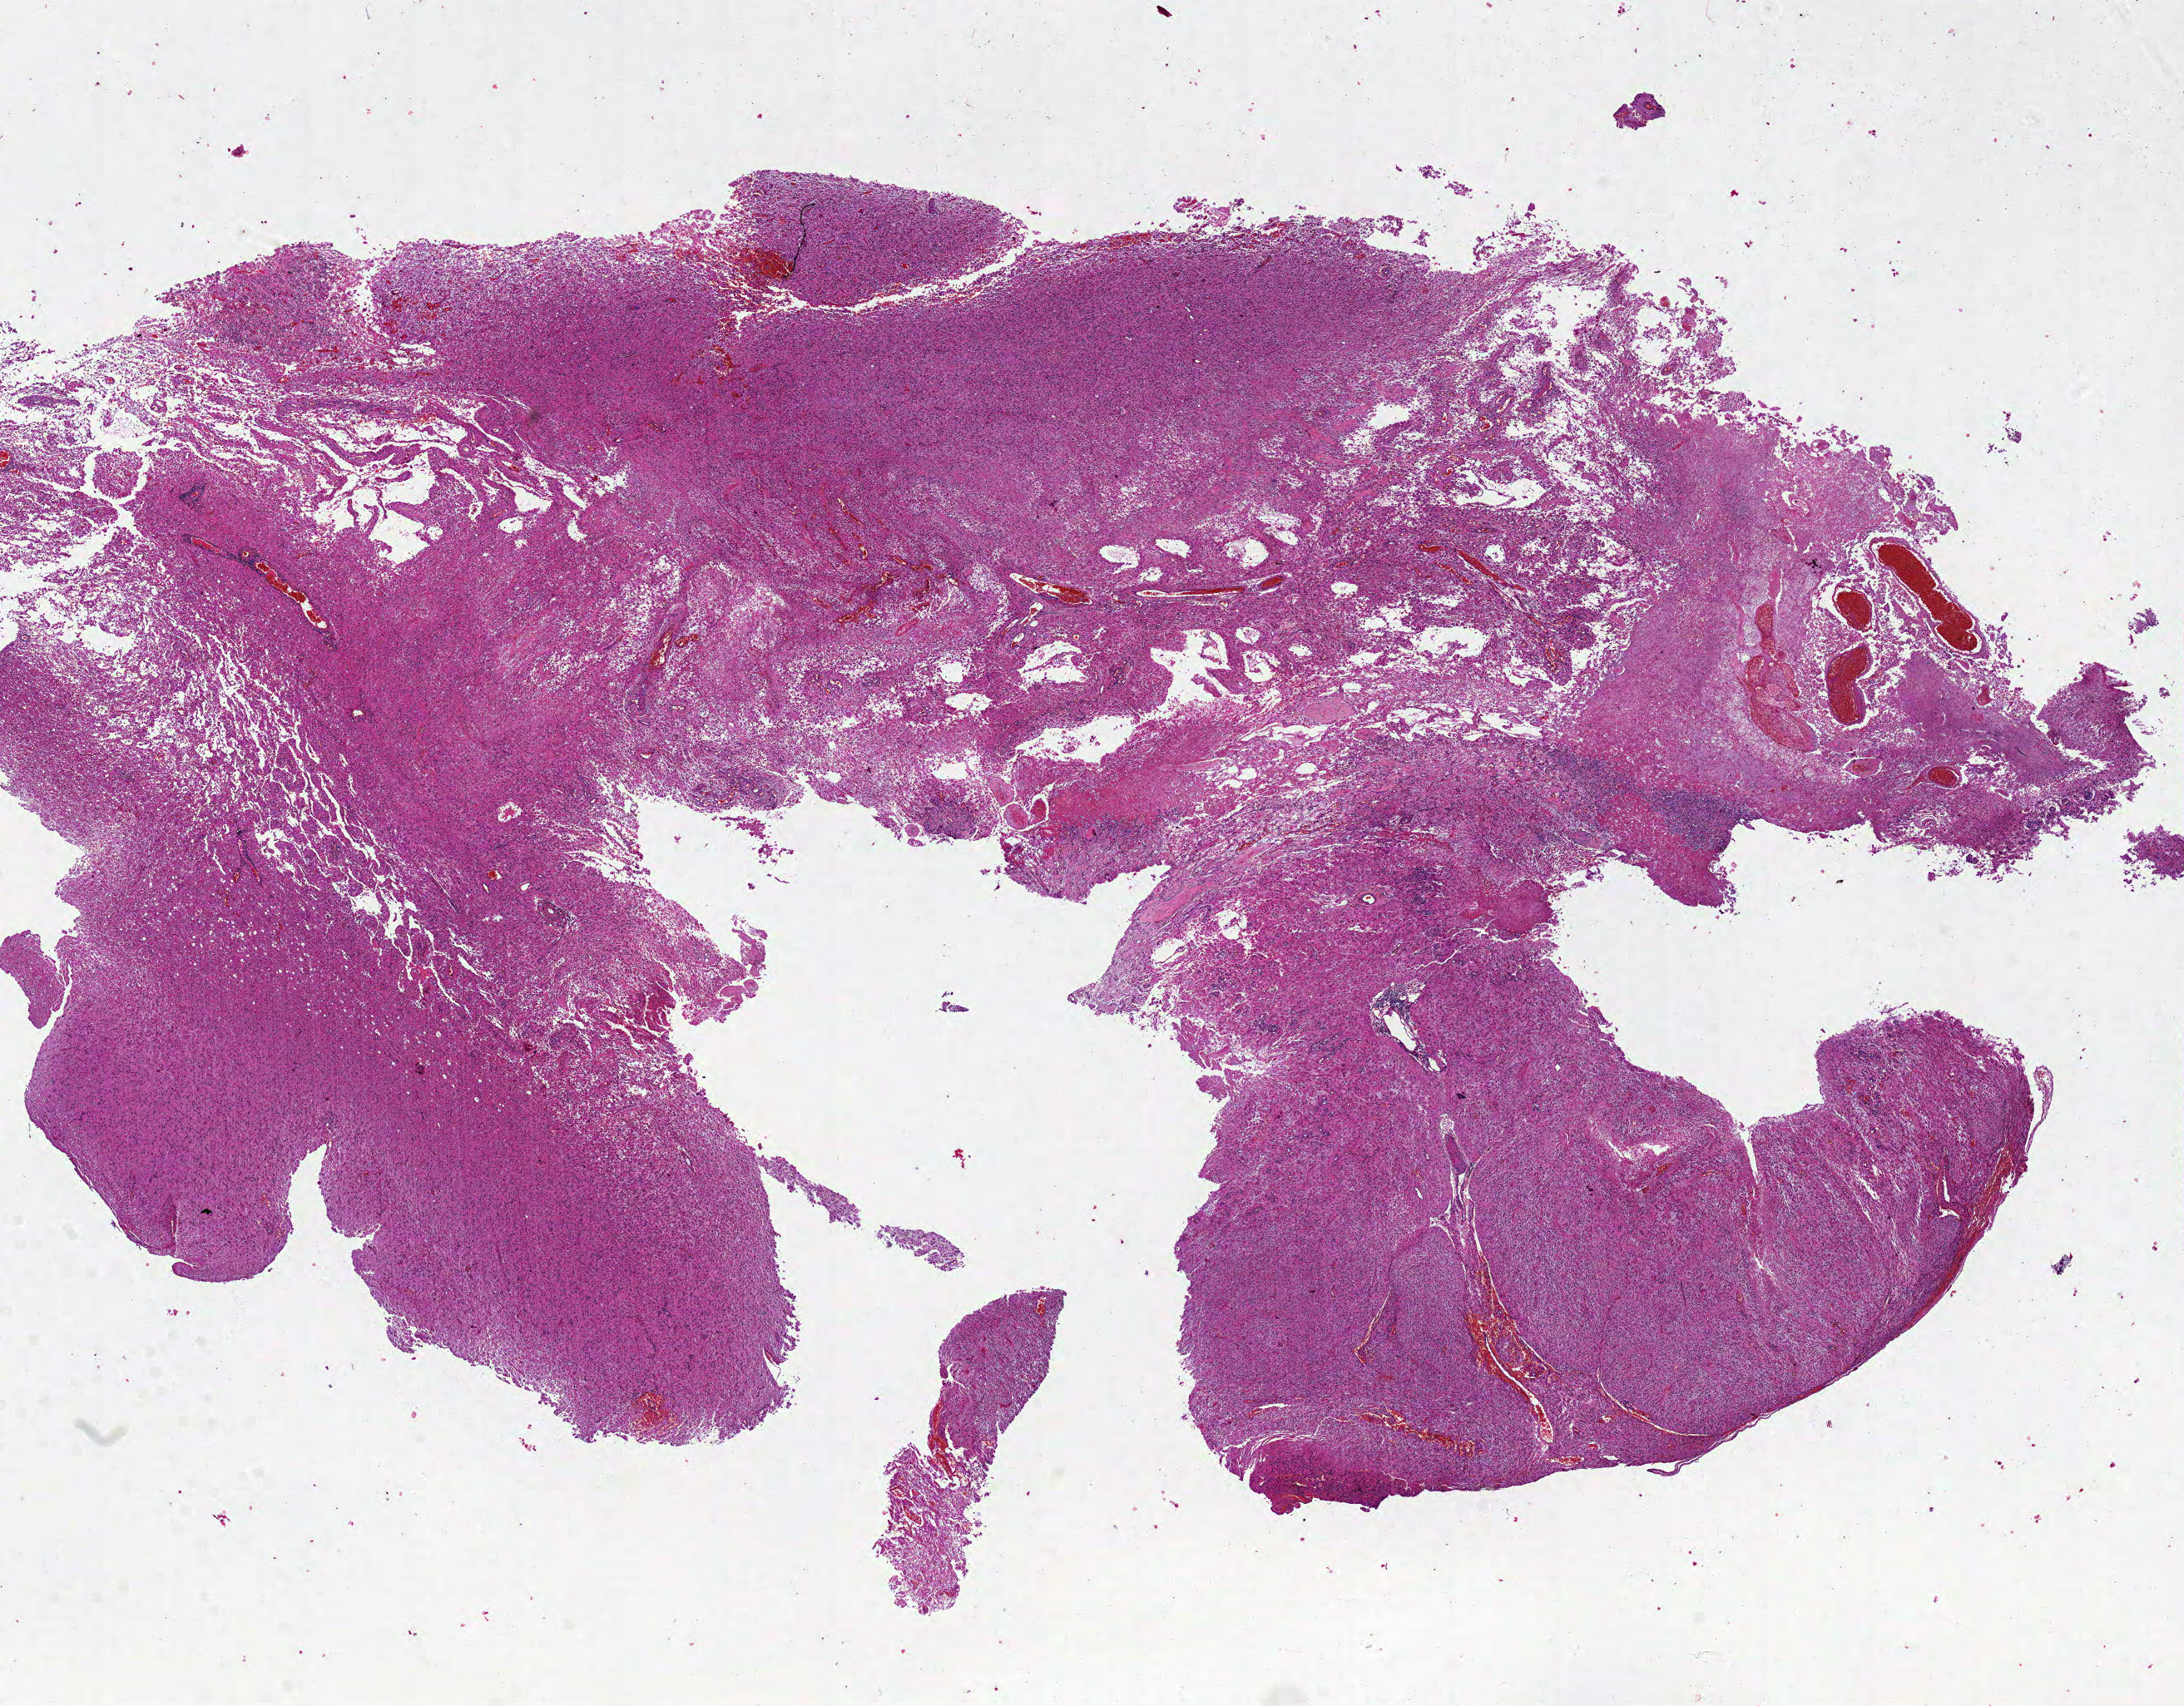
Digitized H&E tissue section (whole slide), low-resolution overview of the scanned area, about 21.0 x 16.4 mm; FFPE section; primary tumour sample from the brain. Patient: male, age at initial diagnosis 57 years.
Histologic diagnosis: Glioblastoma.